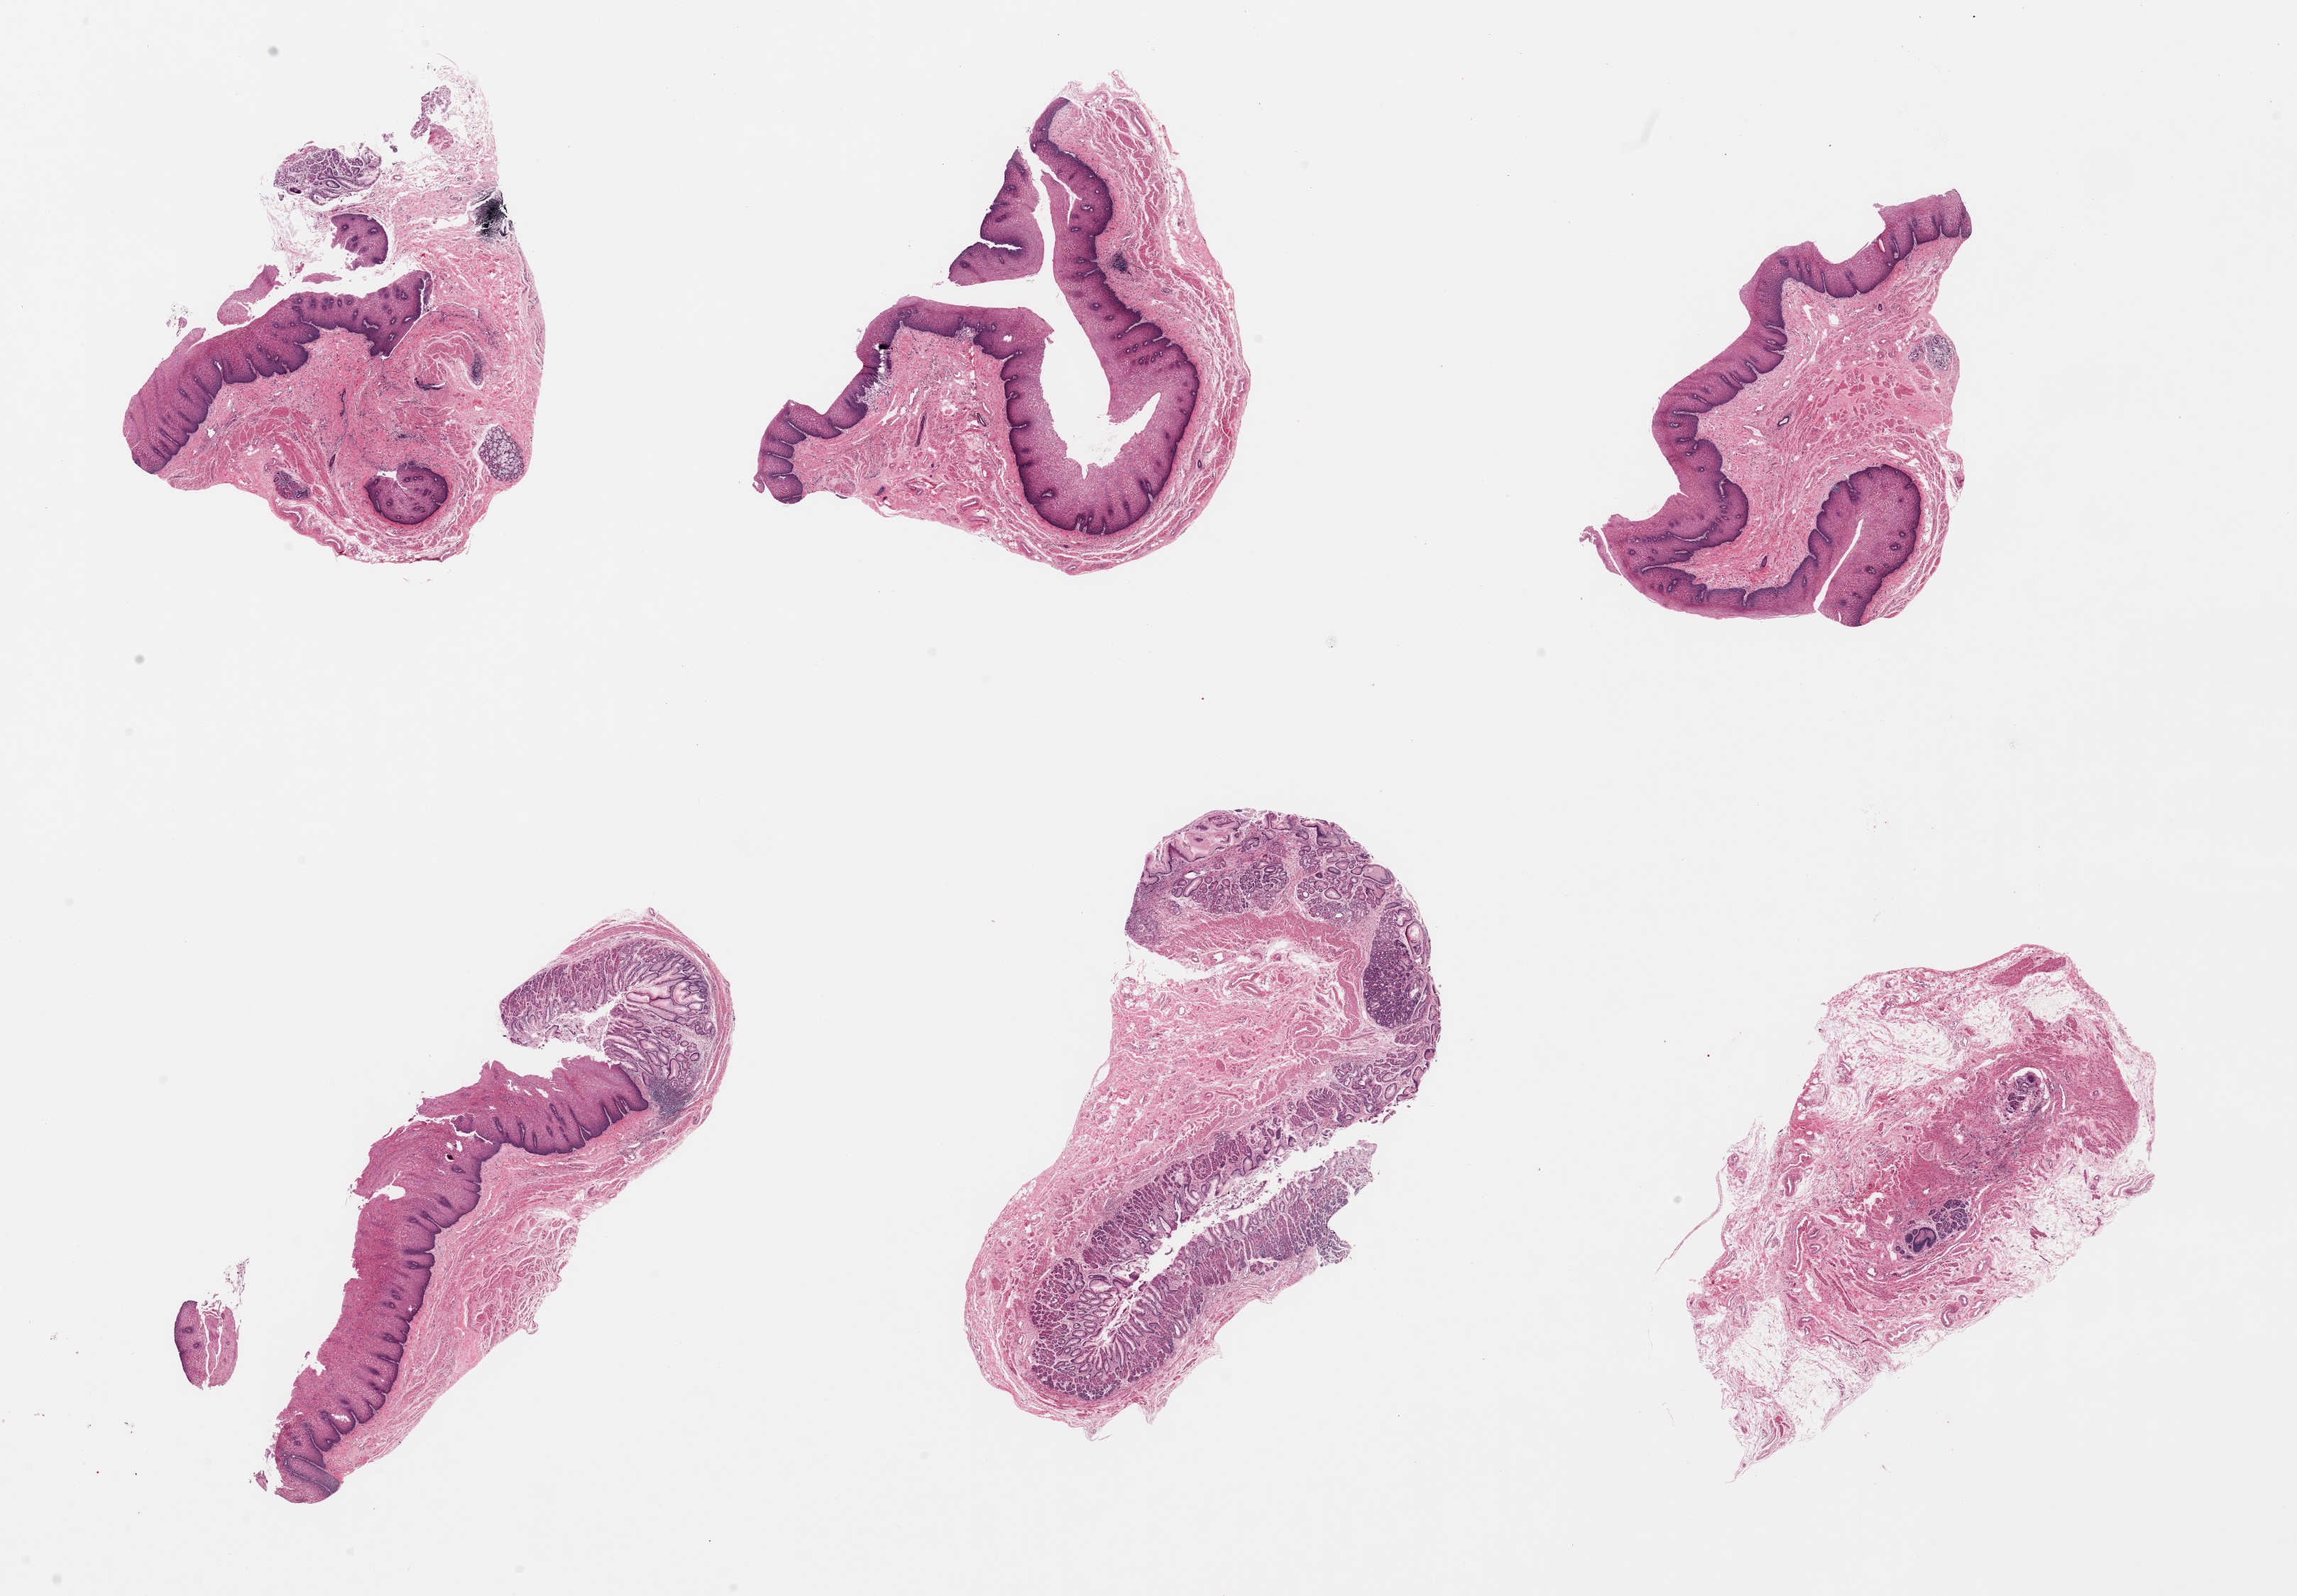
Digitized haematoxylin and eosin-stained section, low-resolution overview of the scanned area, about 25.6 x 17.8 mm, PAXgene-fixed paraffin-embedded (PFPE) section, sampled site (target tissue): gastroesophageal junction, tissue donor sample. Donor: male.
Review note (as recorded): 6 pieces; mucosa (not target), not muscularis.